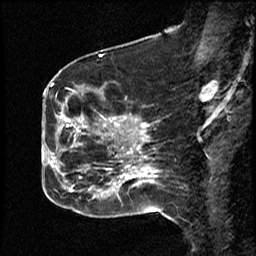
Breast MRI (dynamic contrast-enhanced), one sagittal slice; slice 20 of 50 in the series (ordered by position); dynamic contrast-enhanced study with each time point stored as its own series, time point 2 of 4 at this slice position (early post-contrast, ordered by acquisition time); 1.5 T; TE 4.2 ms, TR 18.5 ms; 3 mm slice thickness; 256 × 256 image matrix, field of view 200 × 200 mm. Patient: female, 44 years. Case-level facts recorded for this patient, not image findings: setting: breast cancer imaged before/during neoadjuvant chemotherapy; receptor status: HR-positive, HER2-negative.
Annotated regions visible in this slice (semi-automatically segmented with operator editing):
- analysis volume of interest (the breast-tissue region the enhancement analysis was run in; not a lesion): box from (x=59, y=83) to (x=114, y=206) px
- tumour enhancement mask (voxels above the 100 % enhancement threshold inside the analysis volume of interest): (x=63, y=117)–(x=91, y=192)